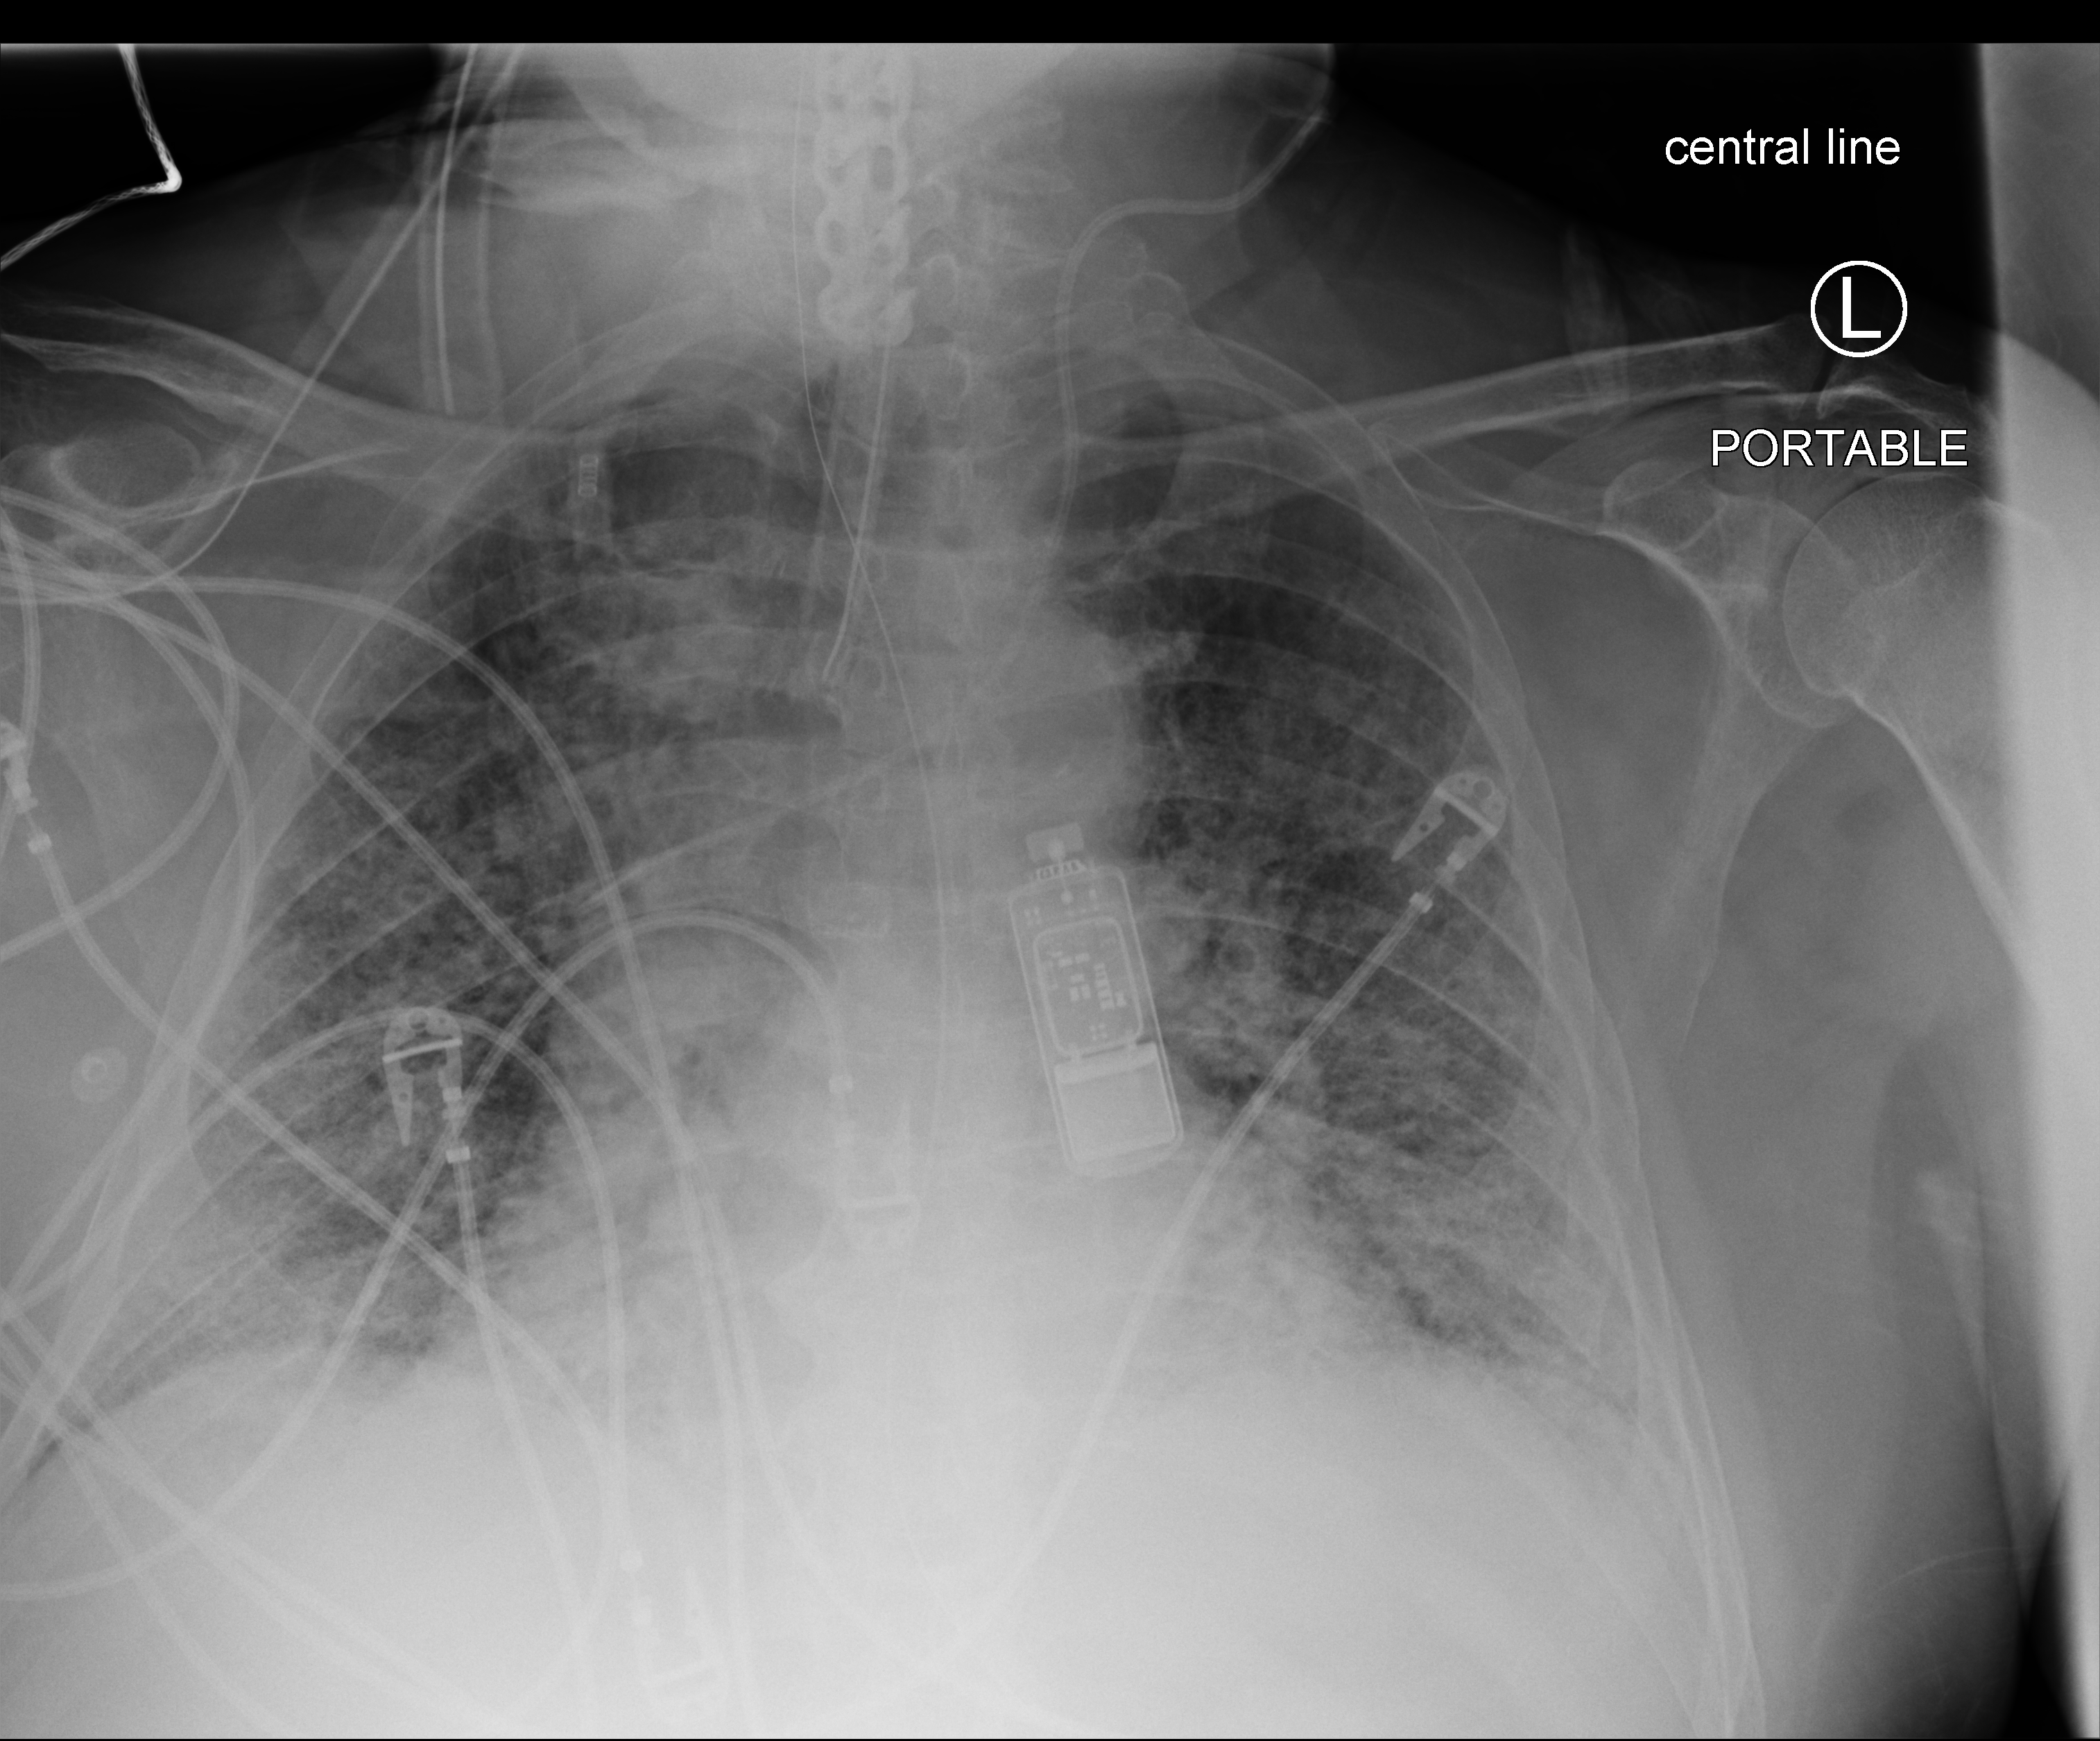
Chest X-ray (portable); anteroposterior (AP) projection. Male patient hospitalised with COVID-19, age 60–74 years.
Hospital-stay facts (about this admission, not read from this image; timing relative to this image not recorded): mechanically ventilated during this hospital stay: yes; length of hospital stay: 7 days.